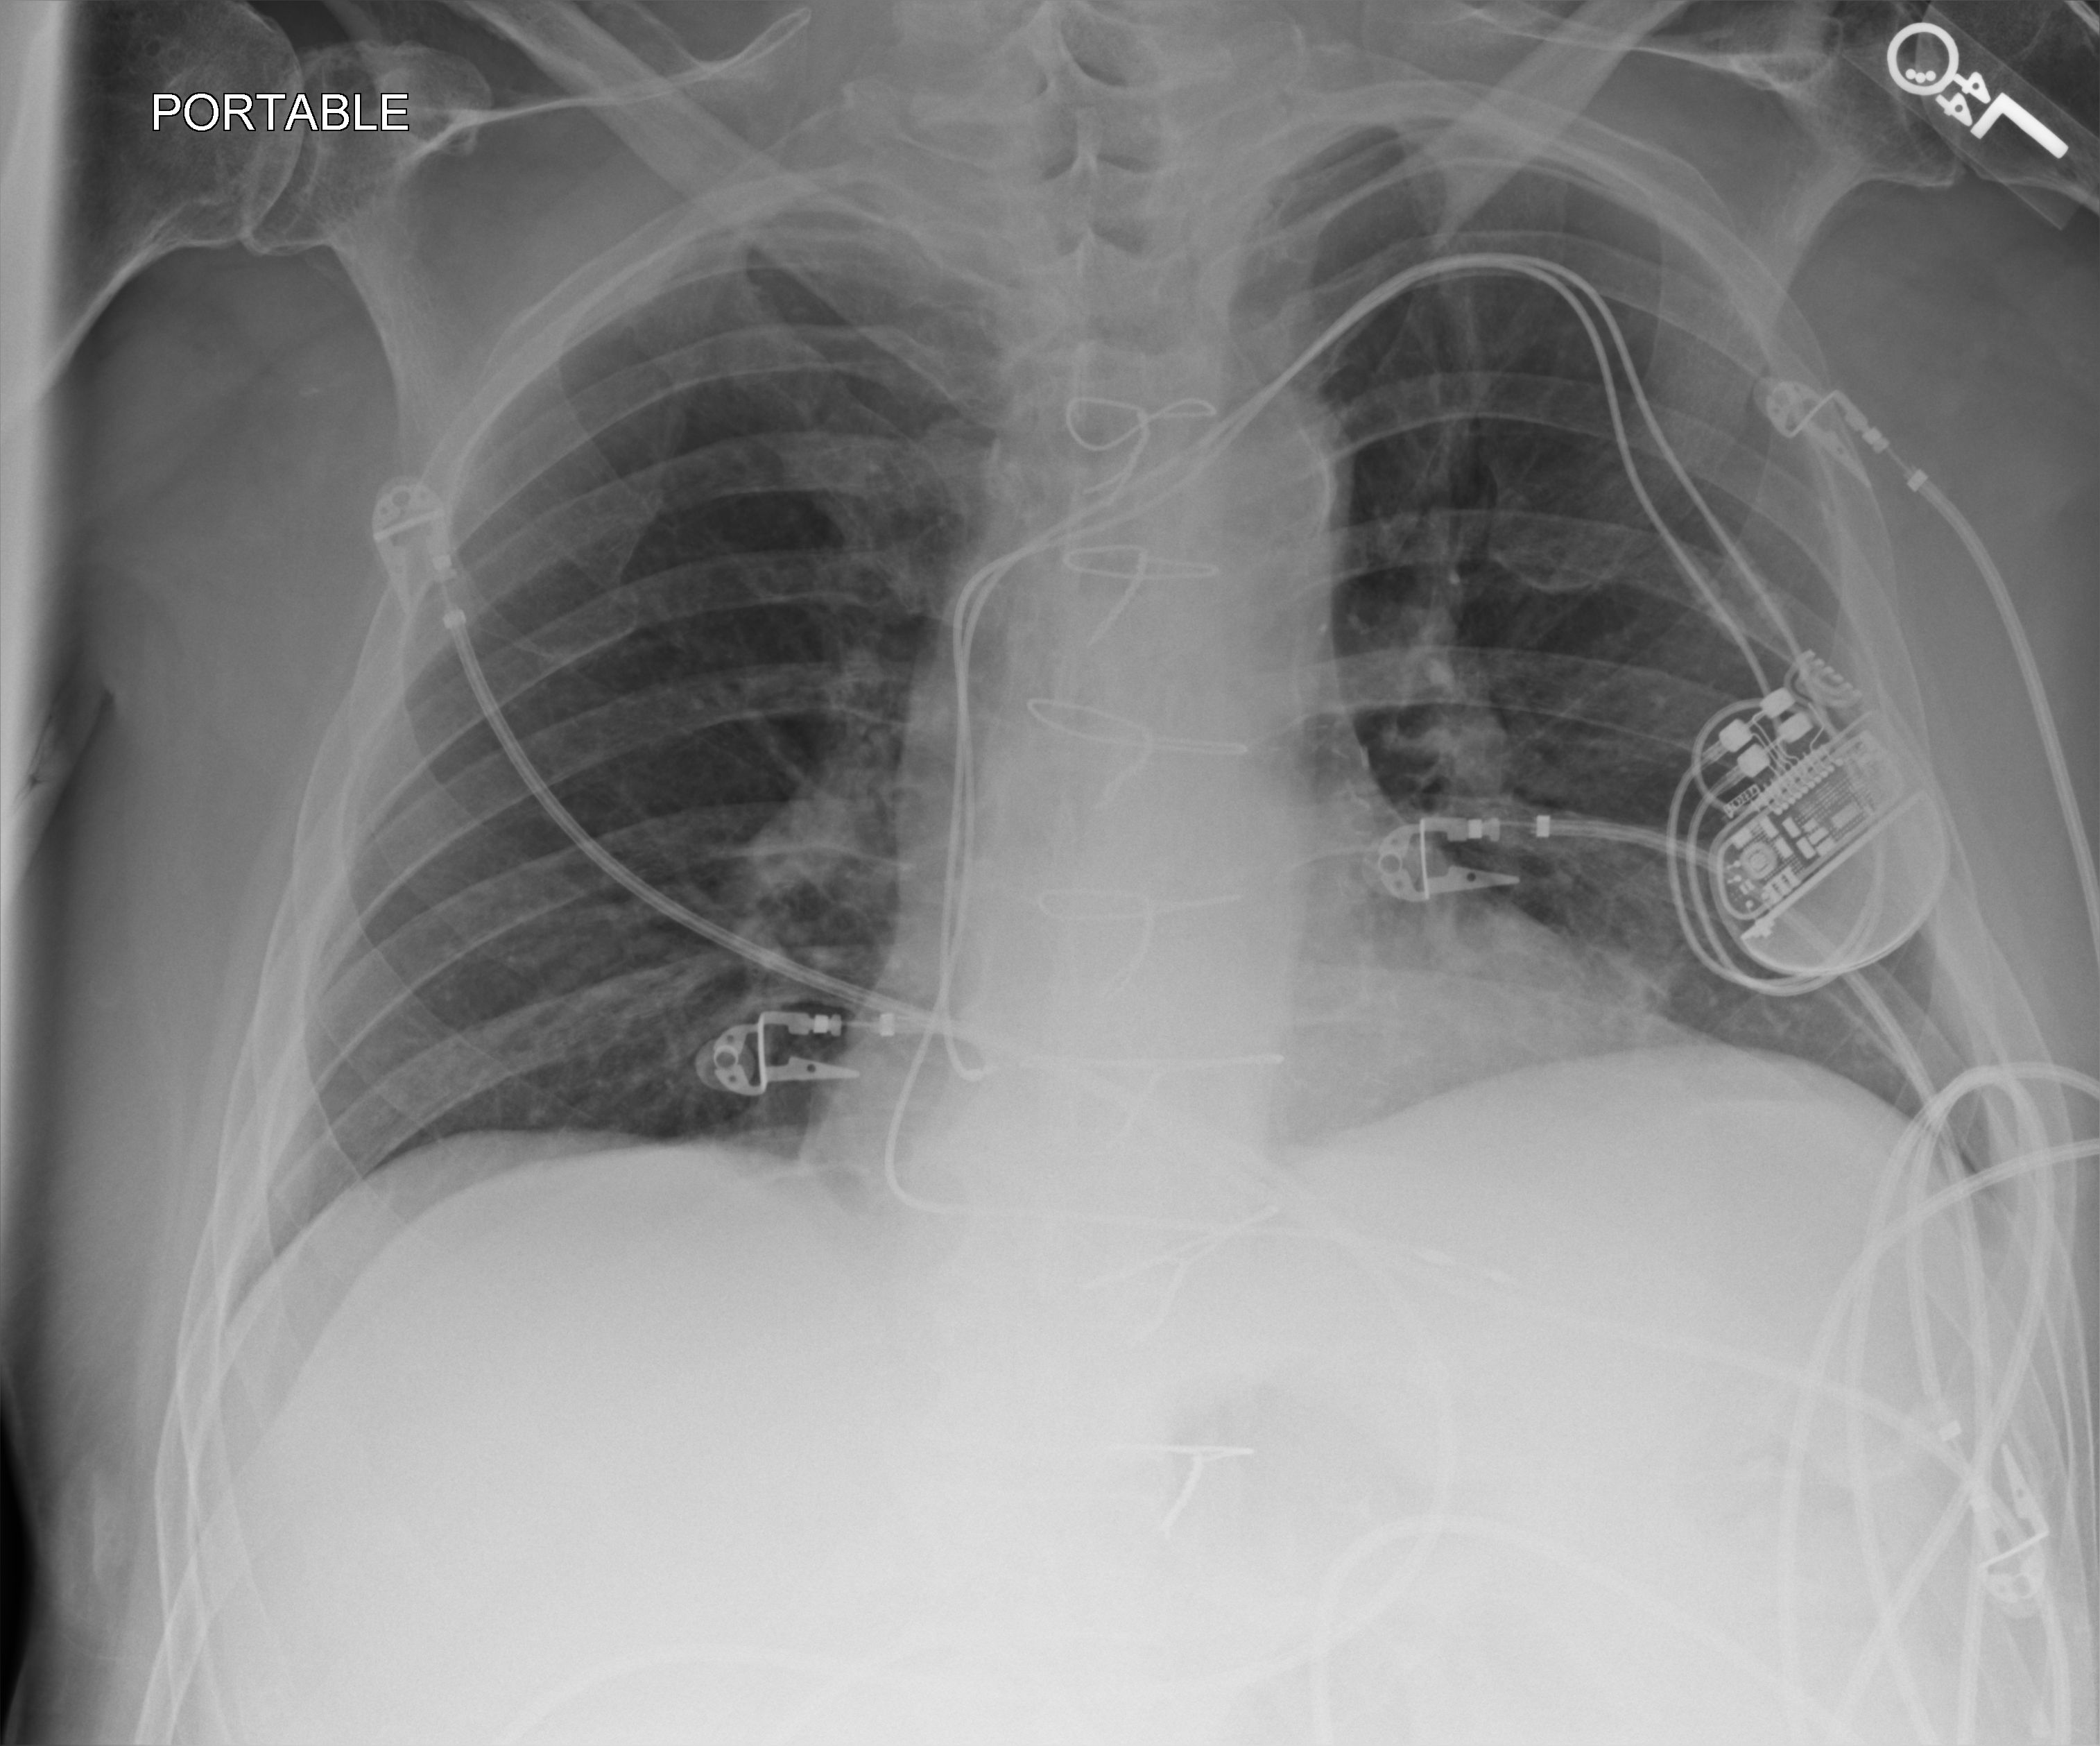
Bedside chest radiograph (computed radiography). Male patient hospitalised with COVID-19, age 75–90 years.
From the hospital-stay record, not from the radiograph (when in the stay this image was taken is not recorded):
- admitted to intensive care during this hospital stay: no